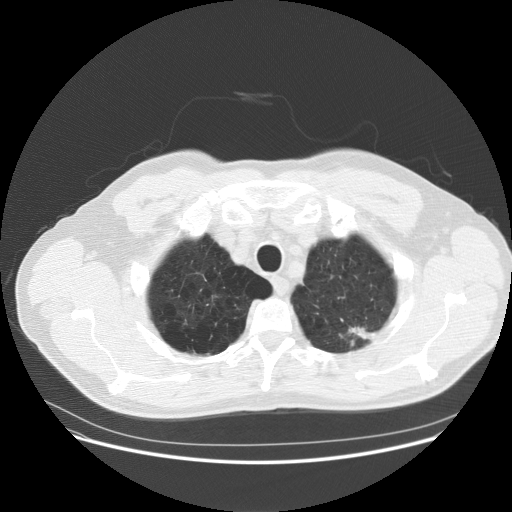
Low-dose screening chest CT, one axial slice. Position 144 of 158 along the scan axis. 120 kVp. Lung window (W 1500 / L -600 HU). 2.5 mm slice thickness. 512 × 512 image matrix.
Annotated regions visible in this slice (manually delineated by an expert):
- lesion 1 (tumor, upper lobe of left lung): box from (x=342, y=327) to (x=377, y=346) px